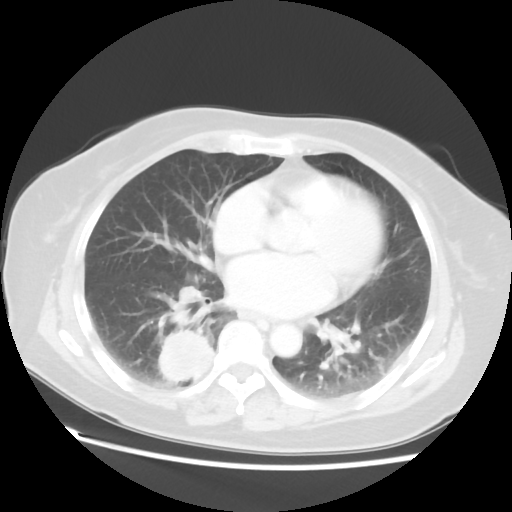
Chest CT, one axial slice; position 26 of 52 along the scan axis; 120 kVp; lung window (W 1500 / L -600 HU); 512 × 512 image matrix. Female patient, age 69 years. Case-level facts recorded for this patient, not image findings: clinical TNM (as recorded): T2 N1 M1a.
Outlined on this slice (rectangle marked by the reading radiologist):
- lung tumour (recorded histology: adenocarcinoma): box from (x=156, y=324) to (x=216, y=386) px